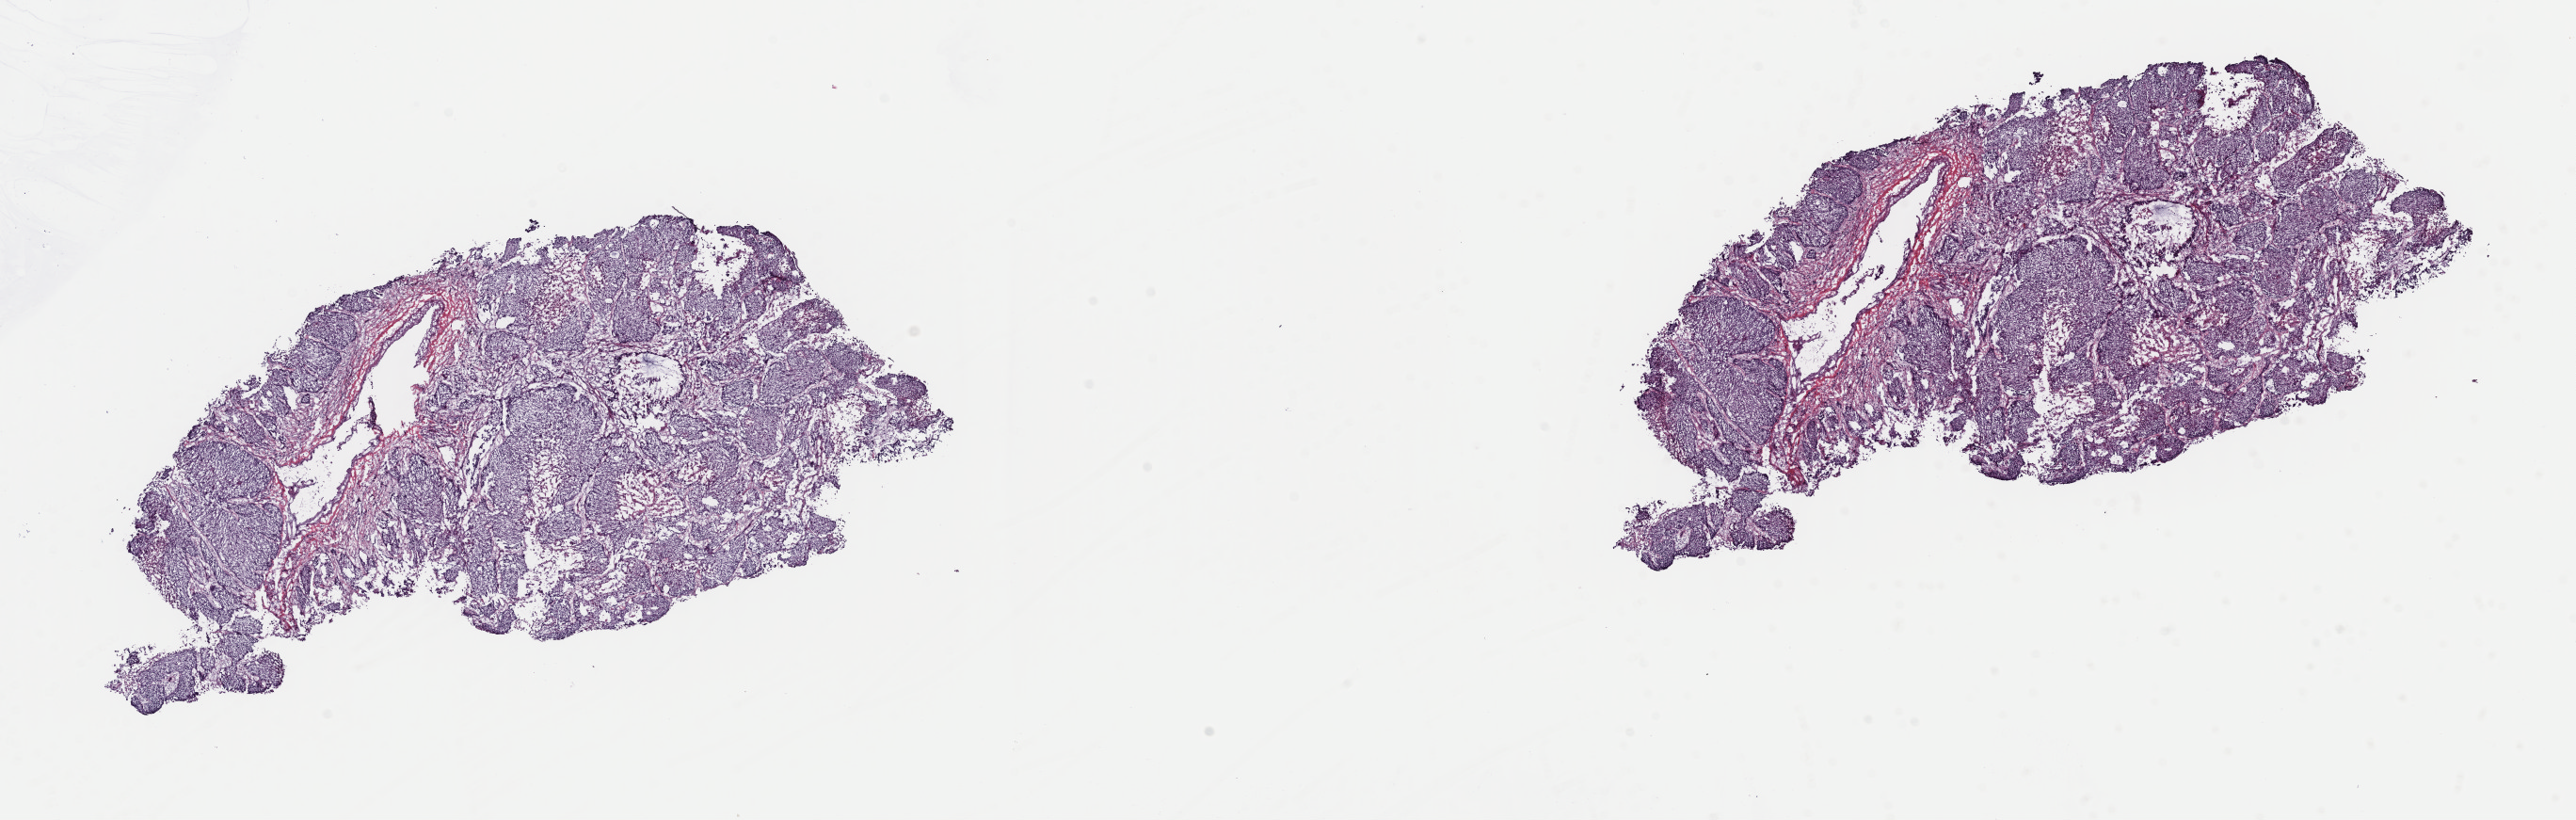
Whole-slide histology image, H&E — shown as a low-resolution overview of the whole scanned area (about 21.6 x 6.9 mm, acquisition: 40x scan), frozen section from the top of the tissue portion, lung, primary tumour sample. Male, age 74 years at initial diagnosis. Pathologist review of this section (percent, as recorded): tumour cells 80%, tumour nuclei 100%, normal cells 0%, stromal cells 15%, necrosis 5%. Infiltration values recorded for this section: lymphocyte infiltration 3%, monocyte infiltration 1%, neutrophil infiltration 0%.
Laterality: left. AJCC pathologic stage: IIIB (6th edition). TNM: T4 N0 MX. Diagnosis: Squamous cell carcinoma, keratinizing, NOS (lower lobe, lung).